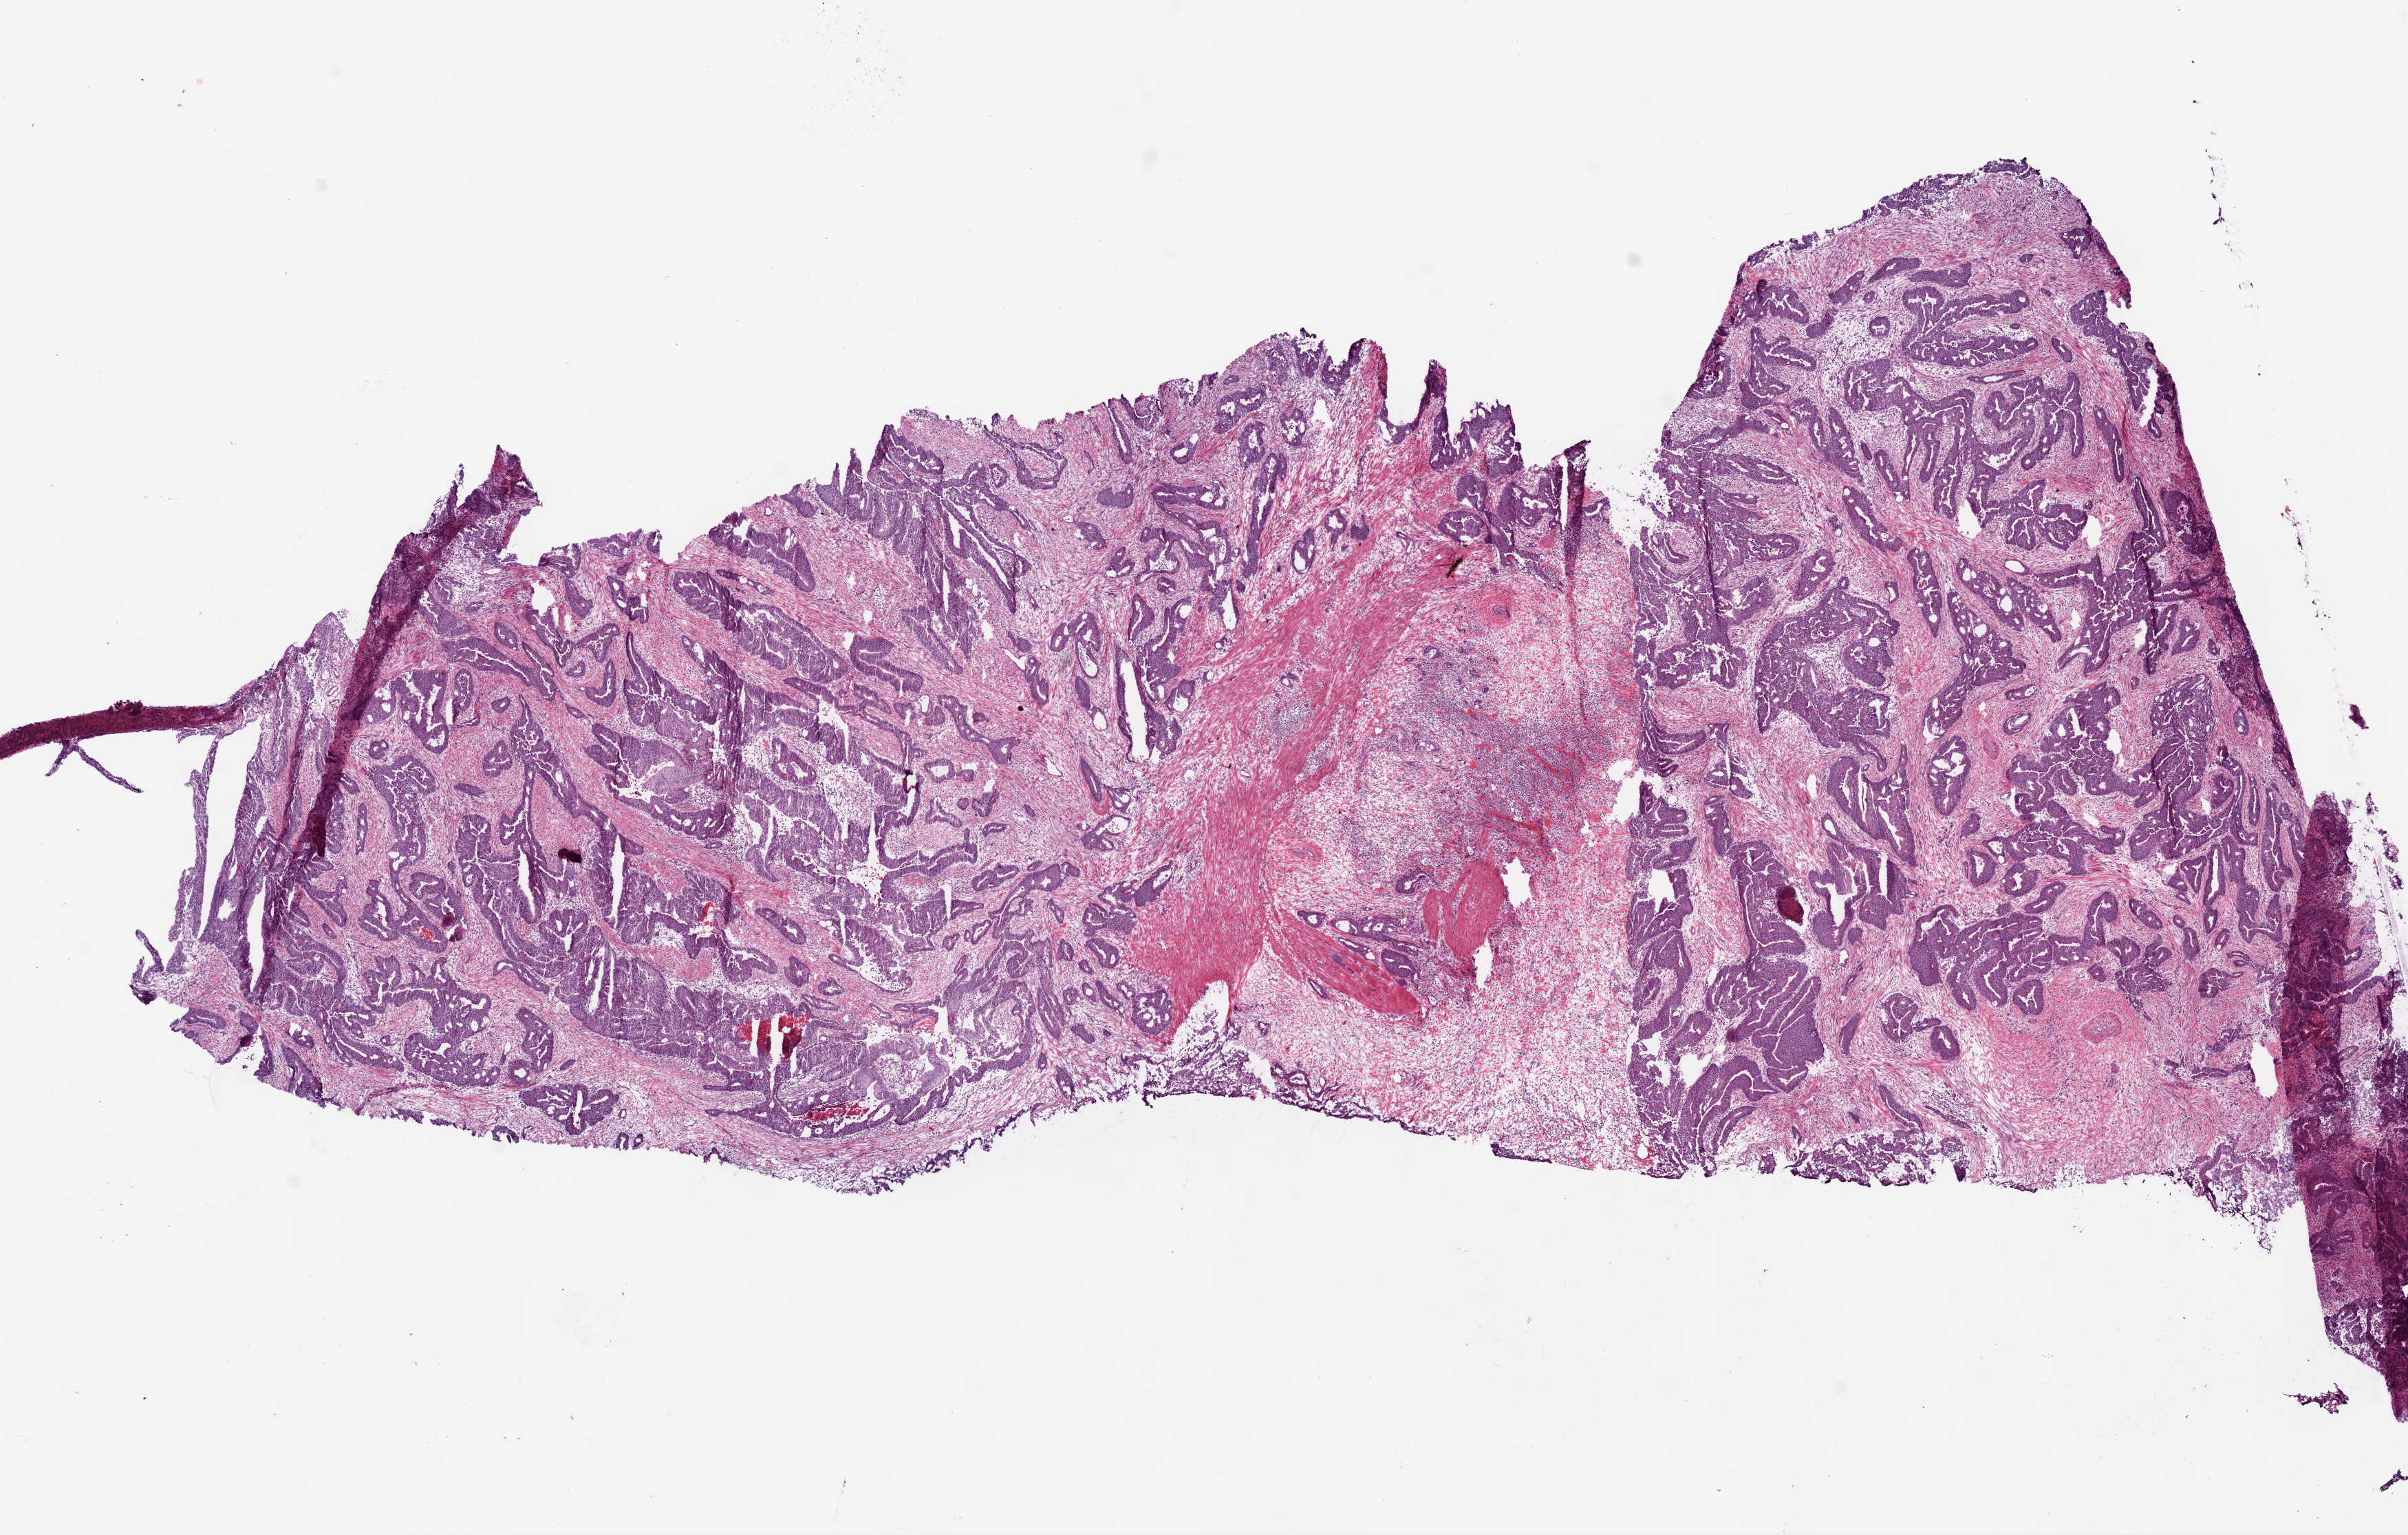
Digitized H&E tissue section (whole slide) — low-resolution overview of the scanned area, about 14.0 x 9.0 mm (from a 20x scan); frozen section; sample: primary tumour, rectum. Male, age 60 years at initial diagnosis. Pathologist review of this section (percent, as recorded): tumour cells 72%, tumour nuclei 70%, normal cells 5%, stromal cells 20%, necrosis 3%.
AJCC pathologic stage: IV. Pathologic diagnosis: Adenocarcinoma, NOS (rectosigmoid junction). TNM: T3 N1 M1. Lymph nodes positive (case pathology): 1 of 26 examined.